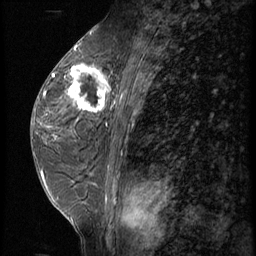
Breast MRI (dynamic contrast-enhanced), one sagittal slice; 3 images stored at this slice position (order not interpretable as contrast timing); 1.5 T; TE 4.2 ms, TR 9 ms; 256 × 256 image matrix, field of view 180 × 180 mm. Female patient, age 44 years. Case-level facts recorded for this patient, not image findings: setting: breast cancer imaged before/during neoadjuvant chemotherapy; receptor status: triple-negative.
Annotated regions visible in this slice (semi-automatic segmentation, software-assisted and operator-edited):
- analysis volume of interest (the breast-tissue region the enhancement analysis was run in; not a lesion): box from (x=67, y=64) to (x=116, y=125) px
- tumour enhancement mask (voxels above the 140 % enhancement threshold inside the analysis volume of interest): (x=67, y=66)–(x=111, y=125)